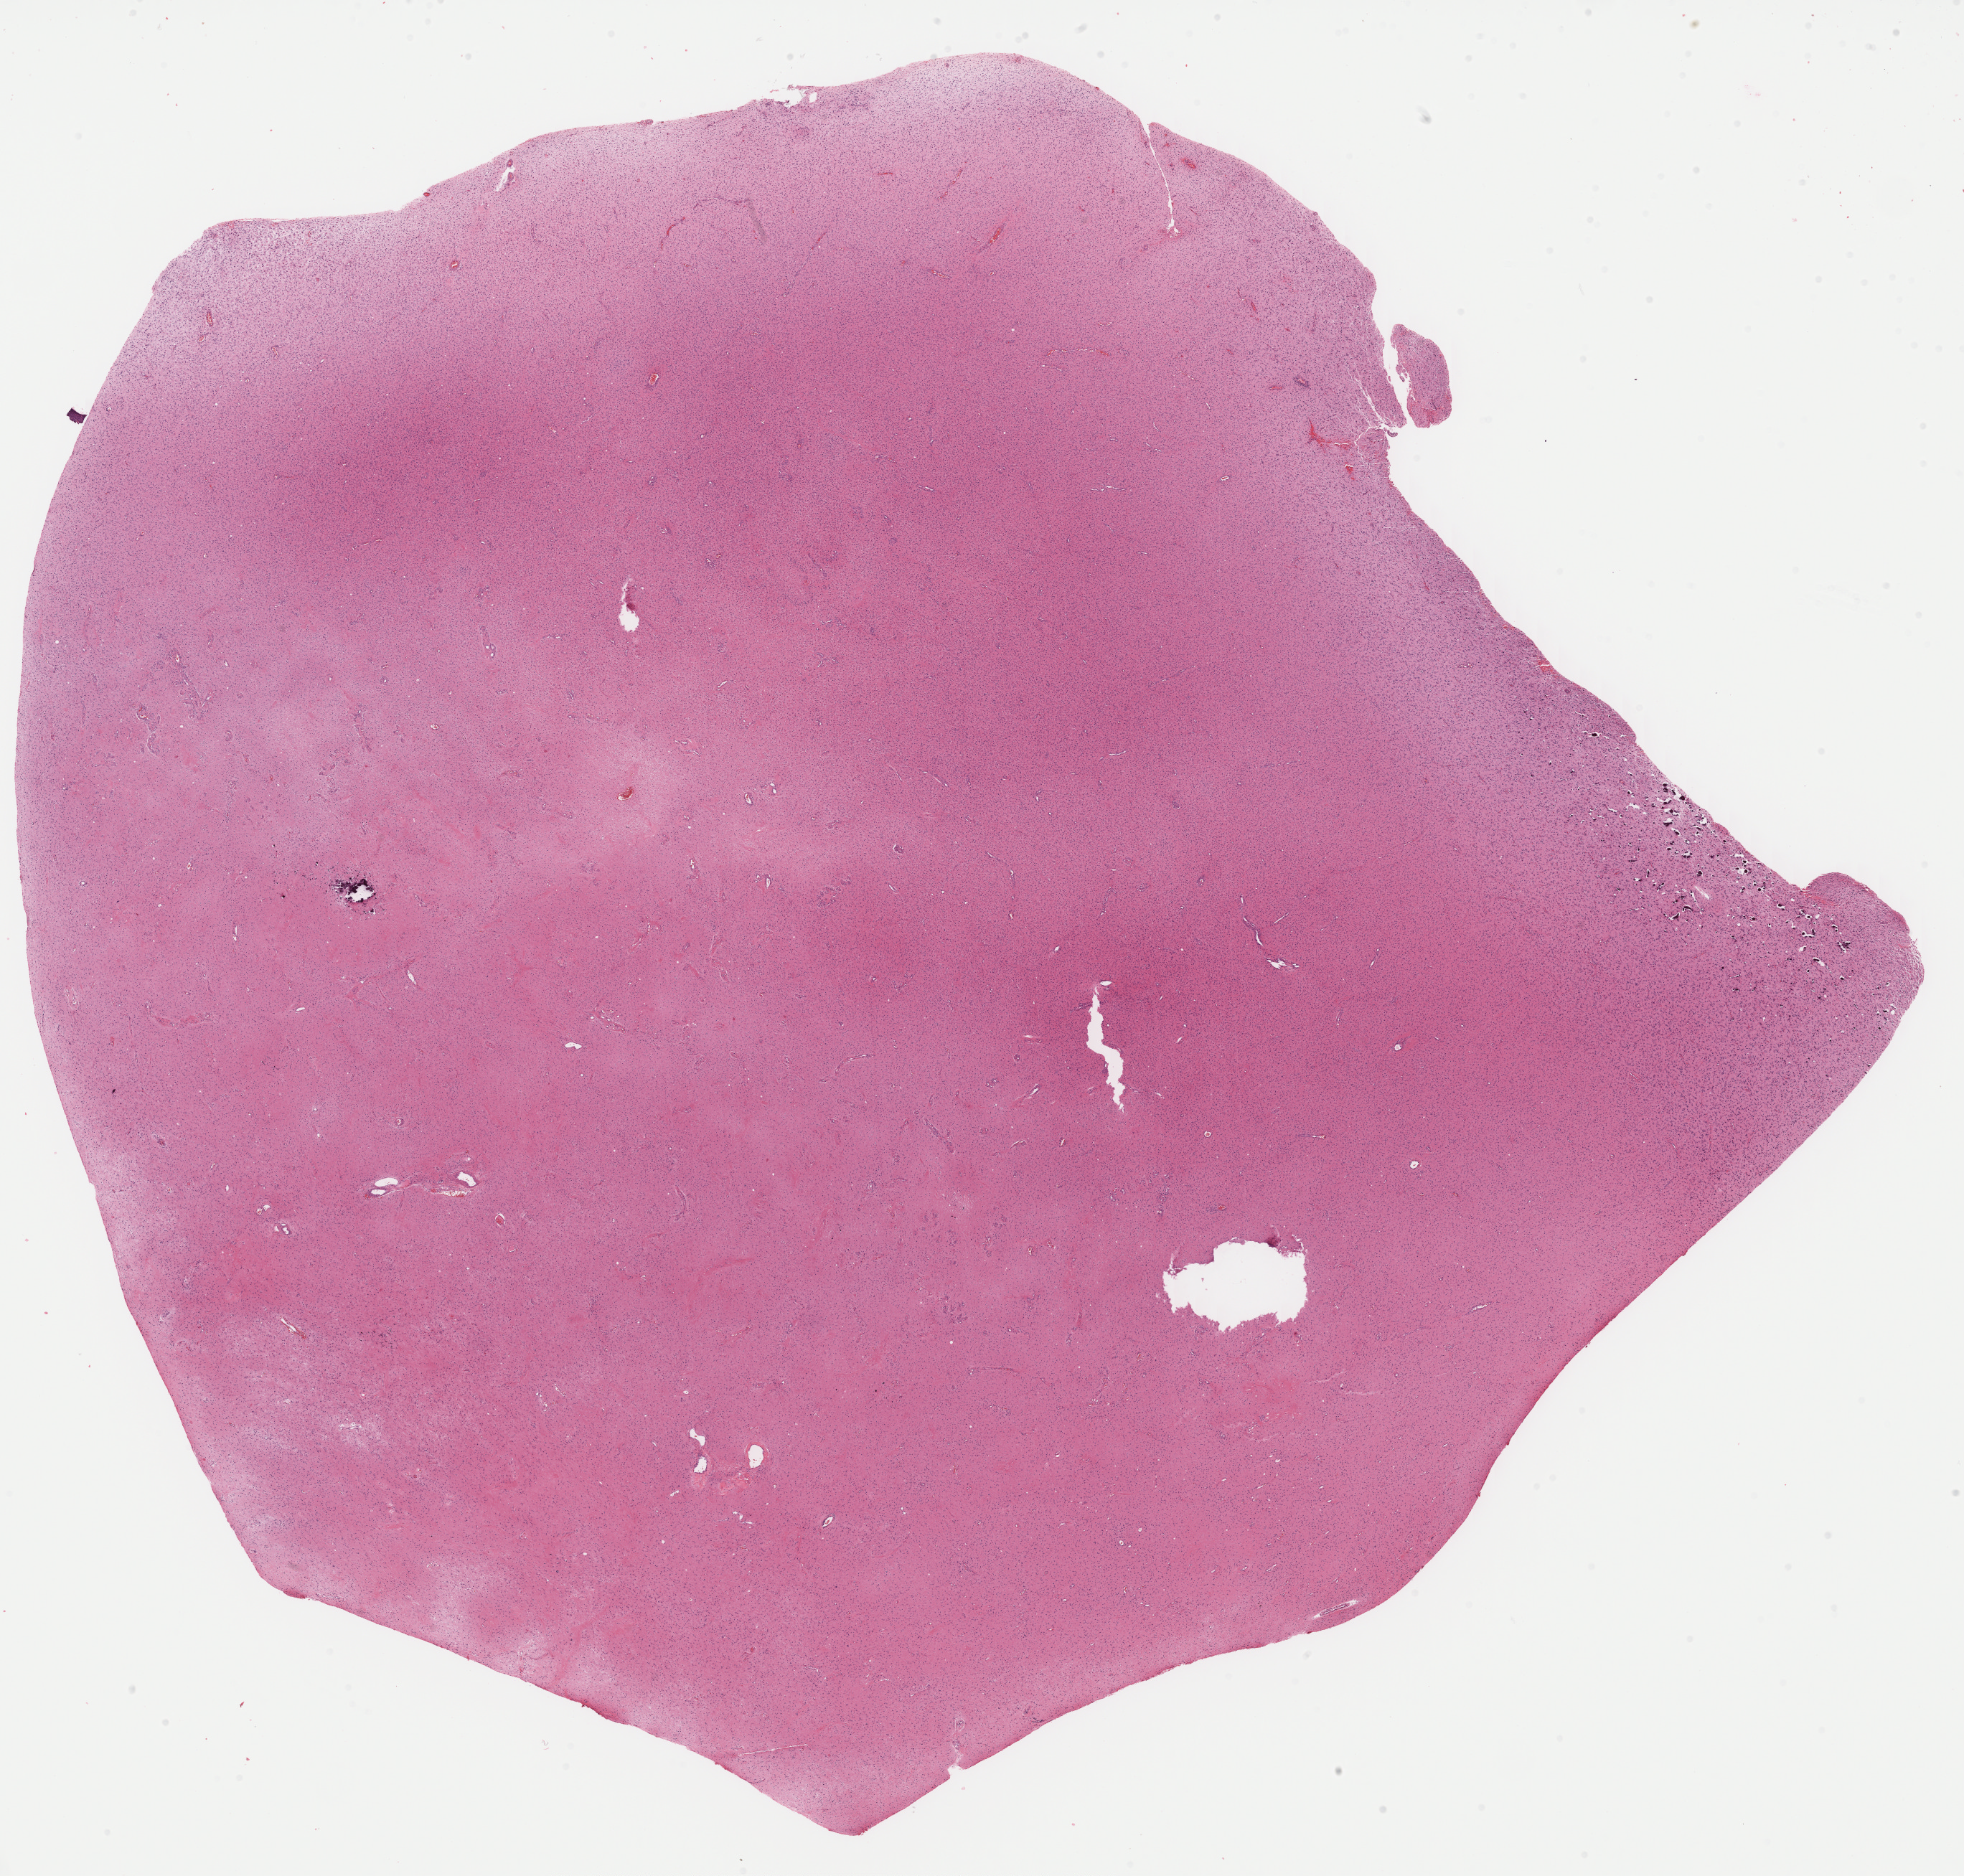
H&E whole-slide image — low-resolution overview of the scanned area, about 21.6 x 20.6 mm. Formalin-fixed paraffin-embedded (FFPE) diagnostic section. Brain, primary tumour sample. Male patient; age at initial diagnosis 33 years. Histologic grade: G3 (poorly differentiated).
- laterality: right
- pathologic diagnosis: Astrocytoma, anaplastic (cerebrum)